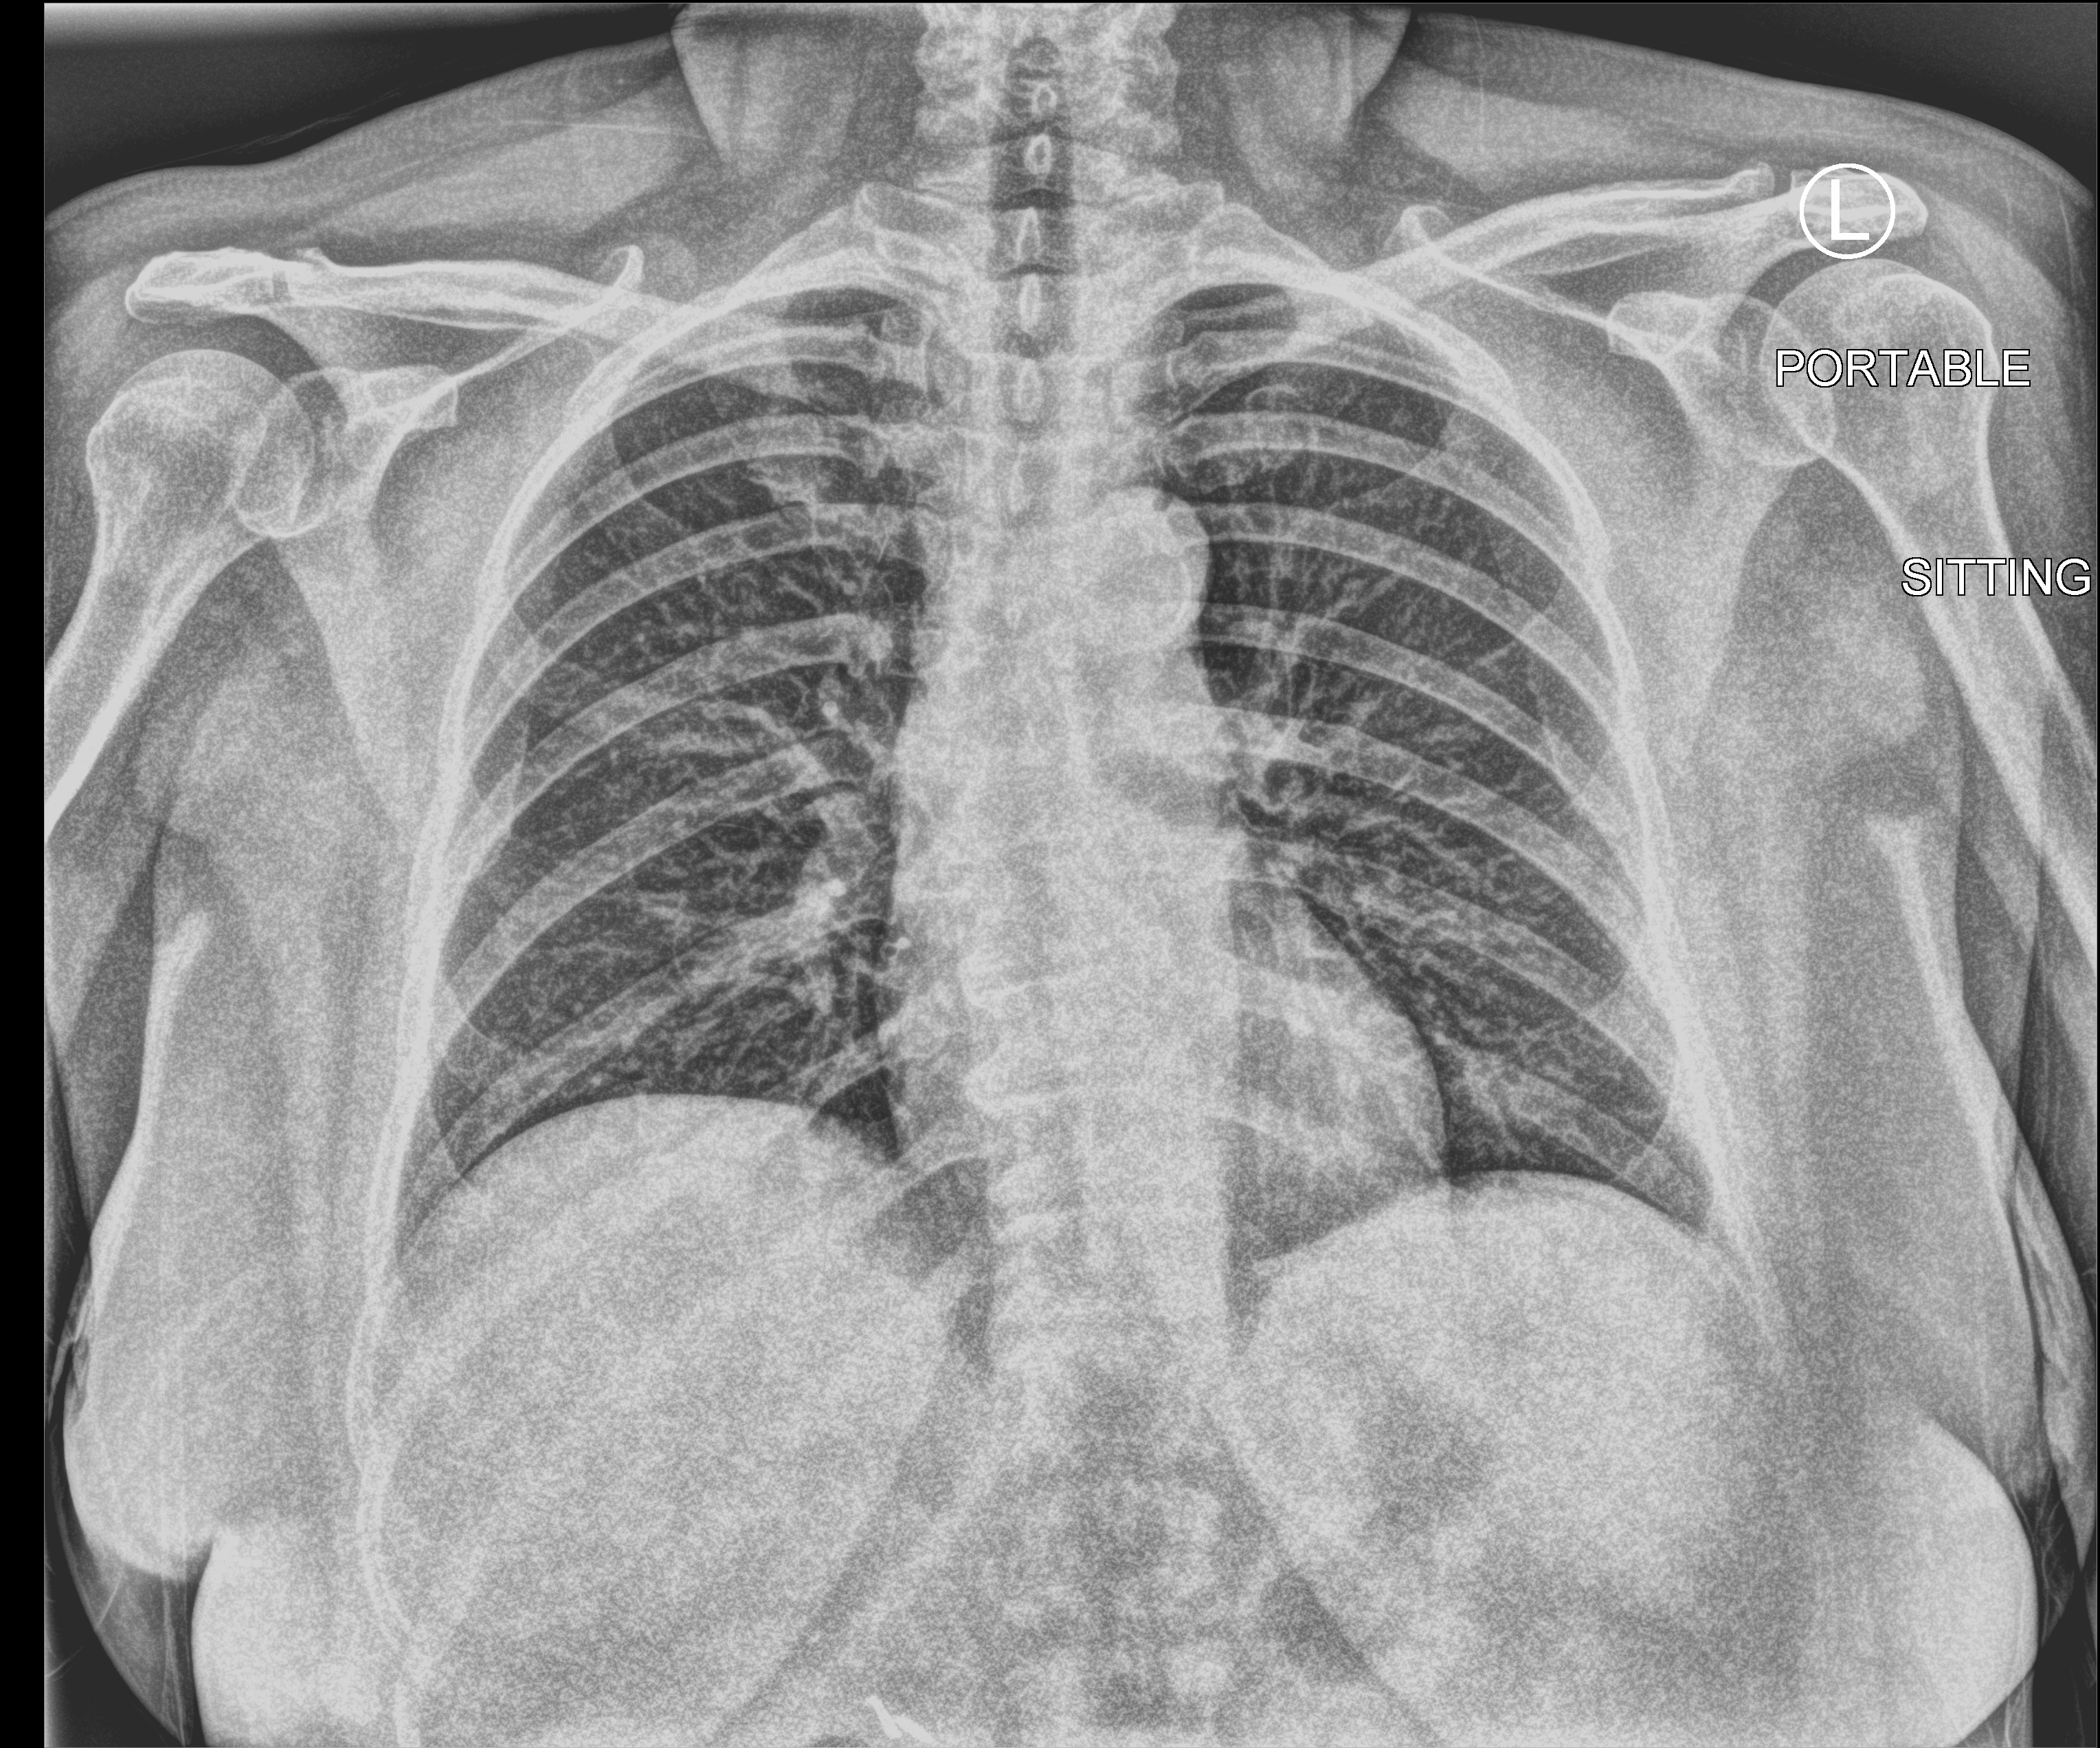
Bedside chest radiograph (computed radiography), anteroposterior (AP) projection. Female patient hospitalised with COVID-19, age 60–74 years.
Hospital-stay facts (about this admission, not read from this image; timing relative to this image not recorded): chronic kidney disease (admission record): no; length of hospital stay: 1 day.